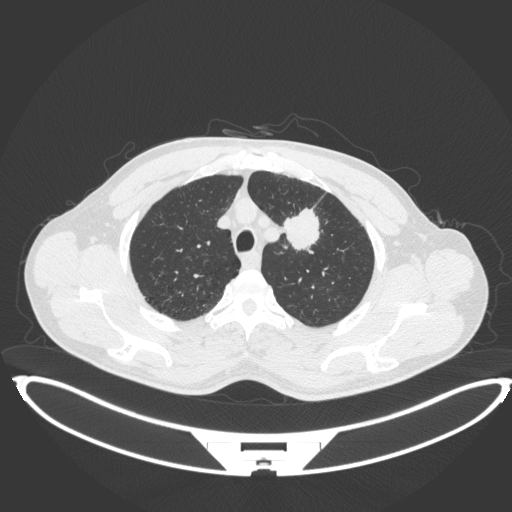
Chest CT, one axial slice. Position 355 of 407 along the scan axis. 120 kVp. Lung window (W 1500 / L -600 HU). 1 mm slice thickness. 512 × 512 image matrix, field of view 457 × 457 mm. Male patient, age 60 years. From the clinical record (not read from this slice): clinical TNM (as recorded): T2a N0 M0.
Structures marked on this image (rectangle marked by the reading radiologist):
- lung tumour (recorded histology: squamous cell carcinoma): bounding box <281,204,322,256> (left, top, right, bottom; pixels)